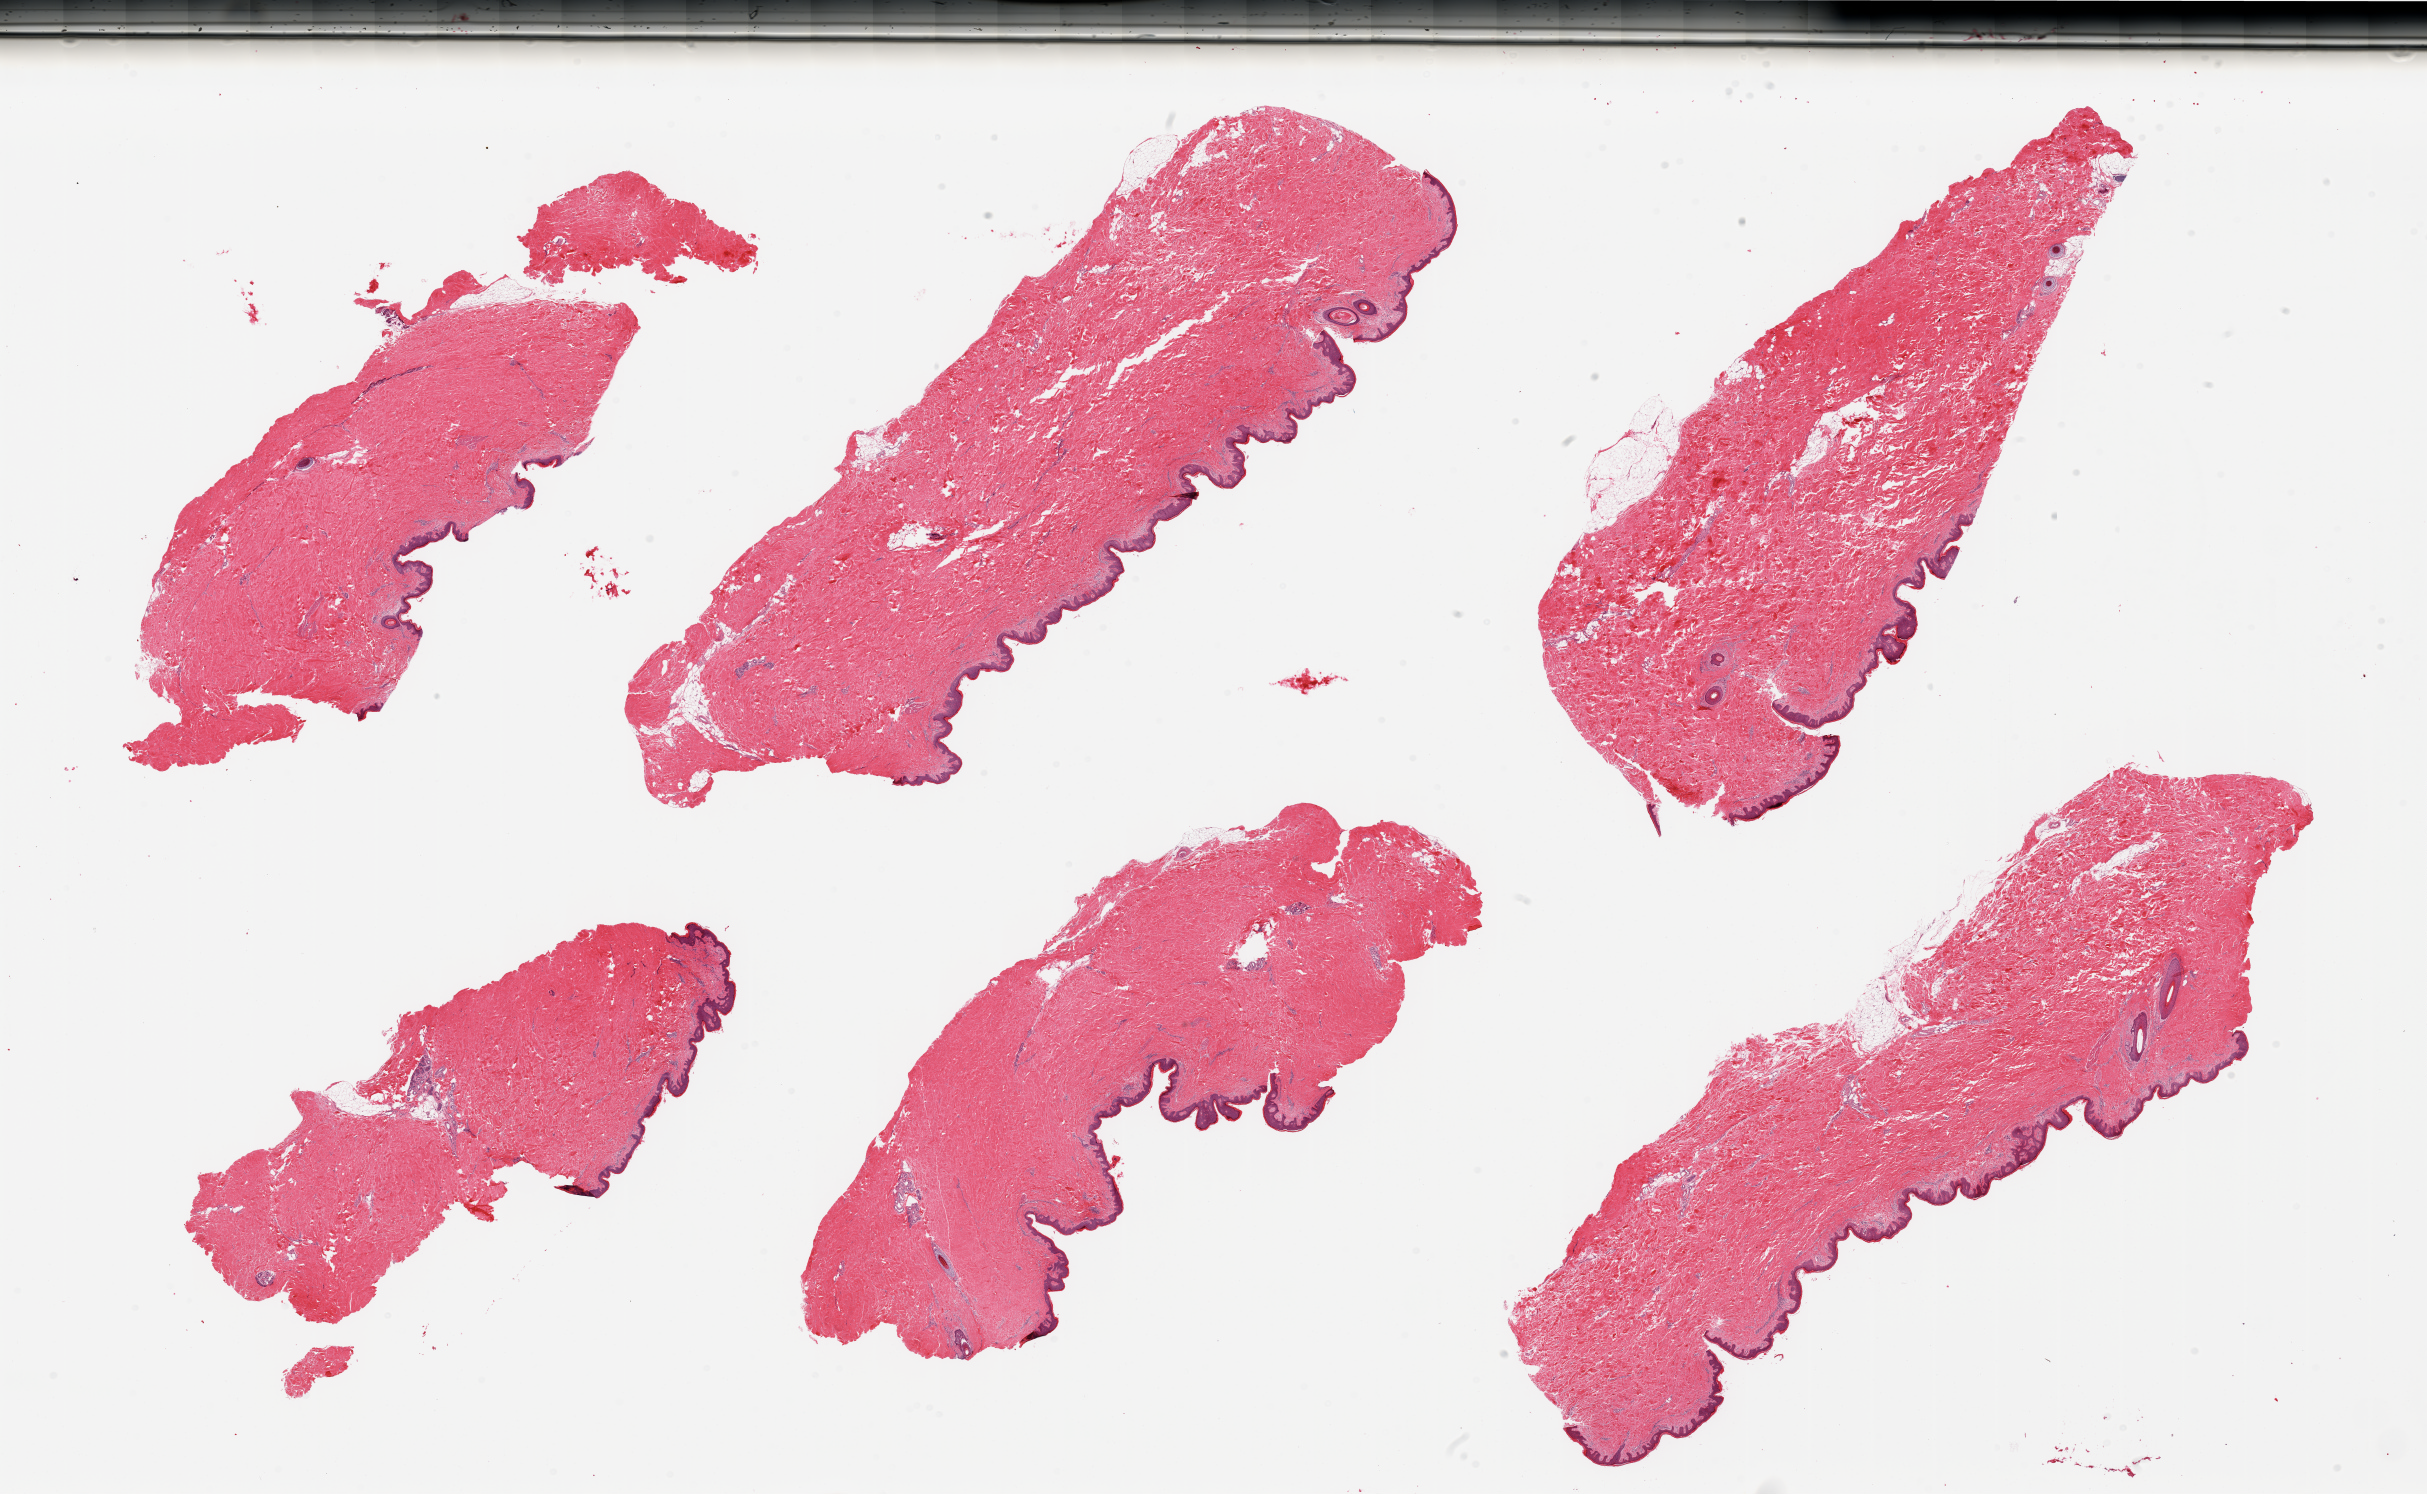
Whole-slide image, hematoxylin and eosin (H&E) stain — whole scanned area (about 38.4 x 23.6 mm) shown as a low-resolution overview; PAXgene-fixed, paraffin-embedded tissue; section of skin of suprapubic region (target tissue); donor tissue sample. Donor: male.
Review note (as recorded): 6 pieces; no intradermal fat; well dissected.